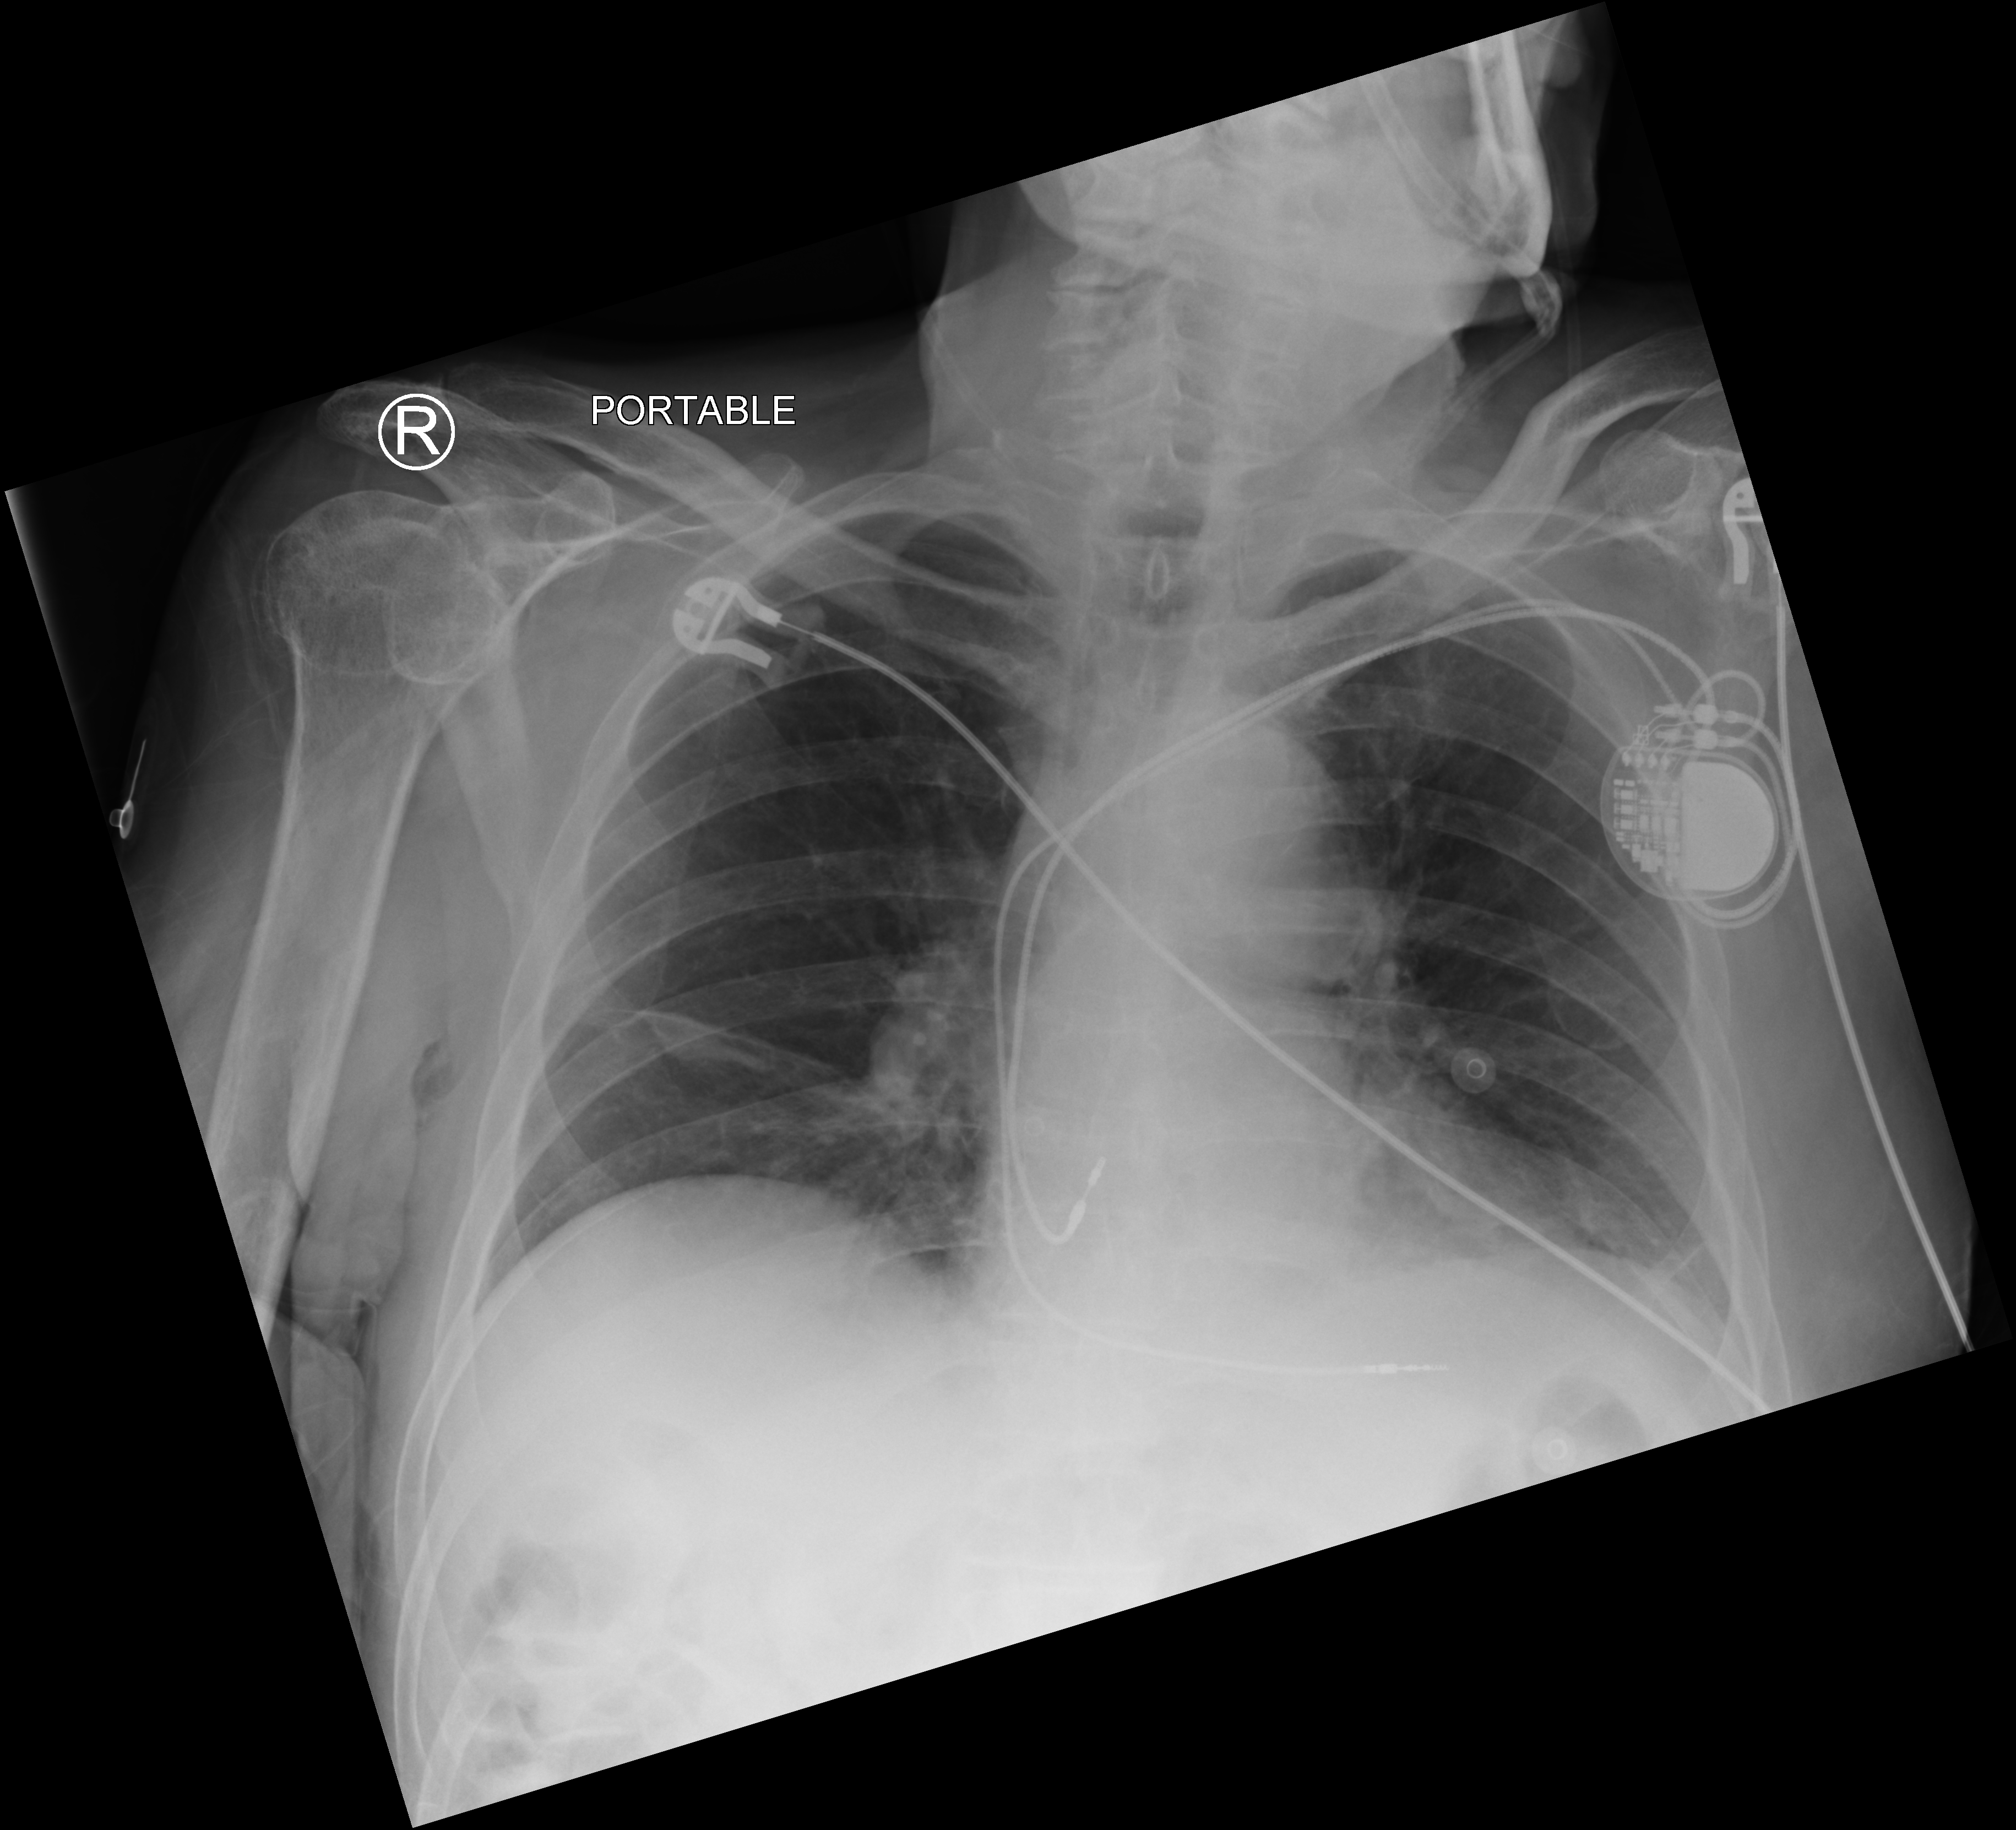
Chest X-ray (portable). Male patient hospitalised with COVID-19, age 60–74 years.
Hospital-stay facts (about this admission, not read from this image; timing relative to this image not recorded):
- chronic kidney disease (admission record): no